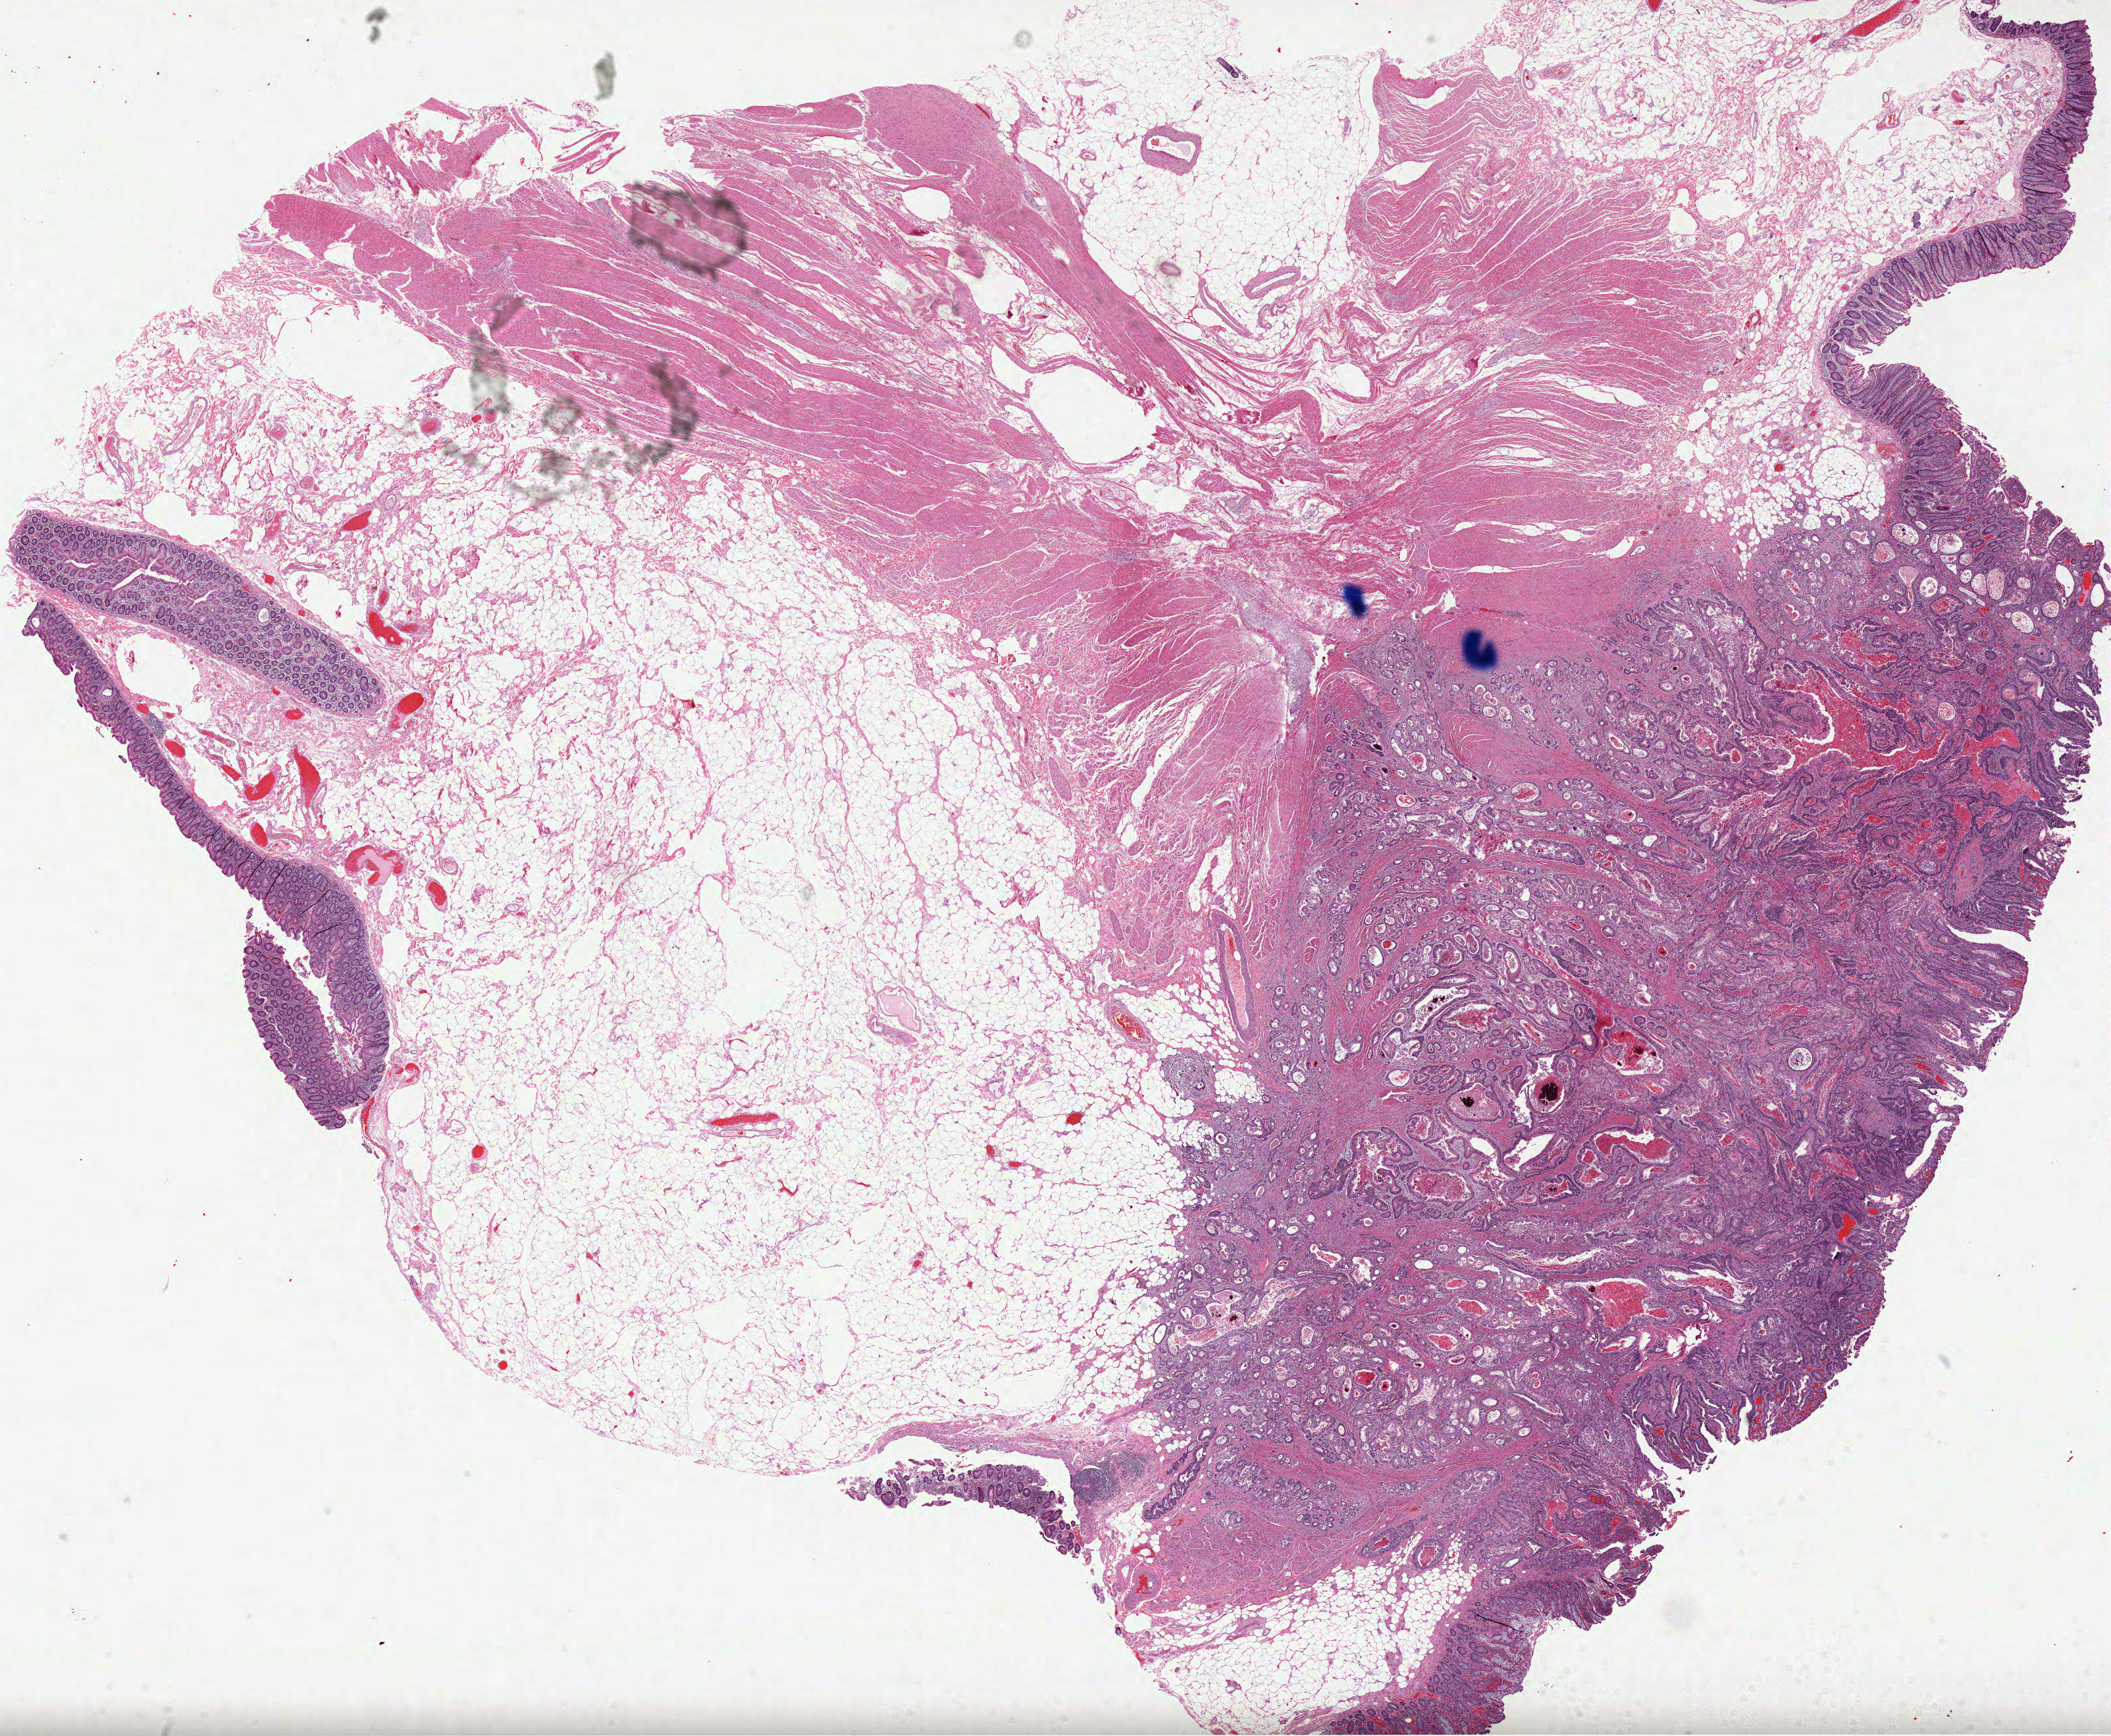
Whole-slide histology image, H&E, low-resolution overview of the scanned area, about 25.9 x 21.3 mm (slide scanned at 40x), formalin-fixed paraffin-embedded (FFPE) diagnostic section, colon, primary tumour sample. Female, age 68 years at initial diagnosis.
• lymph nodes positive (case pathology): 0 of 21 examined
• AJCC pathologic stage: IIA (7th edition)
• pathologic diagnosis: Adenocarcinoma, NOS (cecum)
• TNM: T3 N0 M0